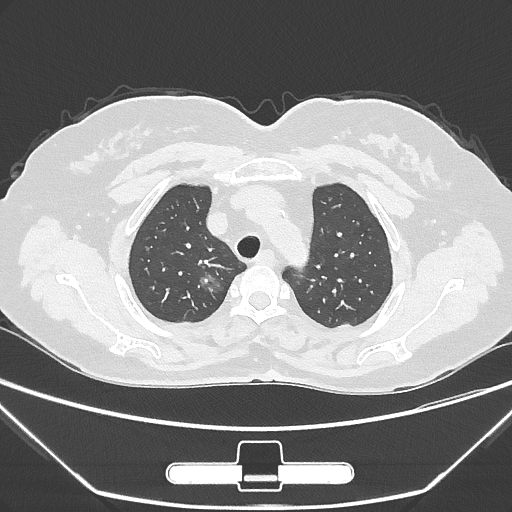
Chest CT, one axial slice; slice 227 of 275 in the series (ordered by position); lung window (W 1500 / L -600 HU); 1 mm slice thickness; 512 × 512 image matrix, field of view 356 × 356 mm. Patient: female, 63 years. Case-level facts recorded for this patient, not image findings: clinical TNM (as recorded): T1a N0 M0; histopathological grade: G1.
Outlined on this slice (bounding box drawn by a radiologist):
- lung tumour (recorded histology: adenocarcinoma): bounding box <193,264,242,309> (left, top, right, bottom; pixels)